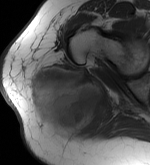
MRI of an extremity soft-tissue mass, one axial slice; slice 35 of 56 in the series (ordered by position); MR volume resampled by the dataset authors to the PET/CT grid (not the native acquisition matrix); 150 × 165 image matrix, field of view 146 × 161 mm. Female patient. Case-level facts recorded for this patient, not image findings: histological type: epithelioid sarcoma with vascular differentiation; site of the primary tumour: right buttock.
Outlined on this slice (expert contour drawn on MRI and transferred to this co-registered scan by the dataset authors):
- gross tumour volume (mass): bounding box (x1, y1, x2, y2) in pixels: (28, 65, 113, 137)